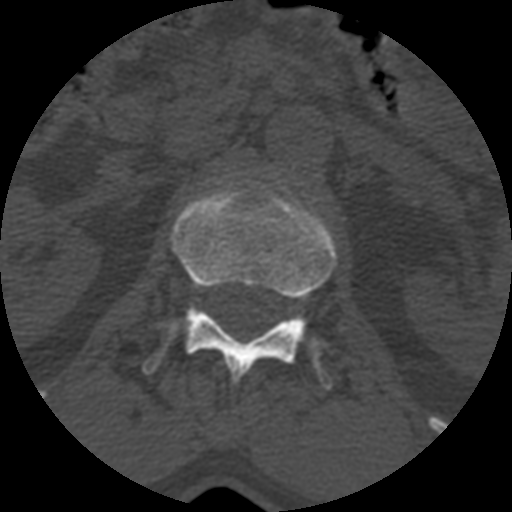
CT including the spine, one axial slice; position 358 of 399 along the scan axis; 120 kVp; bone window (W 1800 / L 400 HU); 1.25 mm slice thickness; 512 × 512 image matrix, field of view 160 × 160 mm. Patient age 71 years. From the clinical record (not read from this slice): primary cancer: prostate.
Annotated regions visible in this slice (semi-automatic segmentation, software-assisted and operator-edited):
- L1 vertebra: bounding box (x1, y1, x2, y2) in pixels: (144, 184, 335, 388)